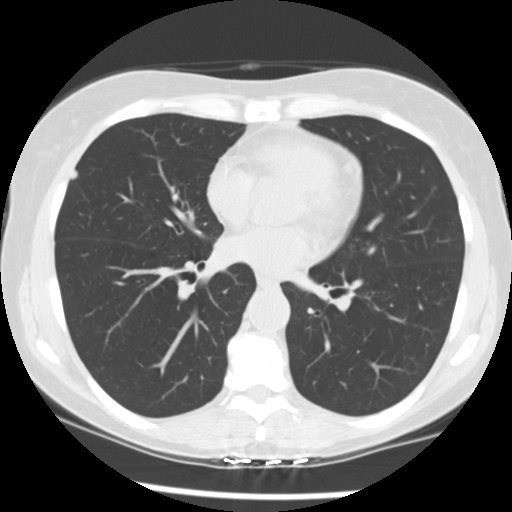
Low-dose screening chest CT, one axial slice; slice 126 of 241 in the series (ordered by position); reconstruction kernel STANDARD; lung window (W 1500 / L -600 HU); 2.5 mm slice thickness; 512 × 512 image matrix, field of view 320 × 320 mm.
Structures marked on this image (expert manual segmentation):
- lesion 1 (tumor, upper lobe of right lung): bounding box [x1, y1, x2, y2] px = [70, 169, 78, 180]